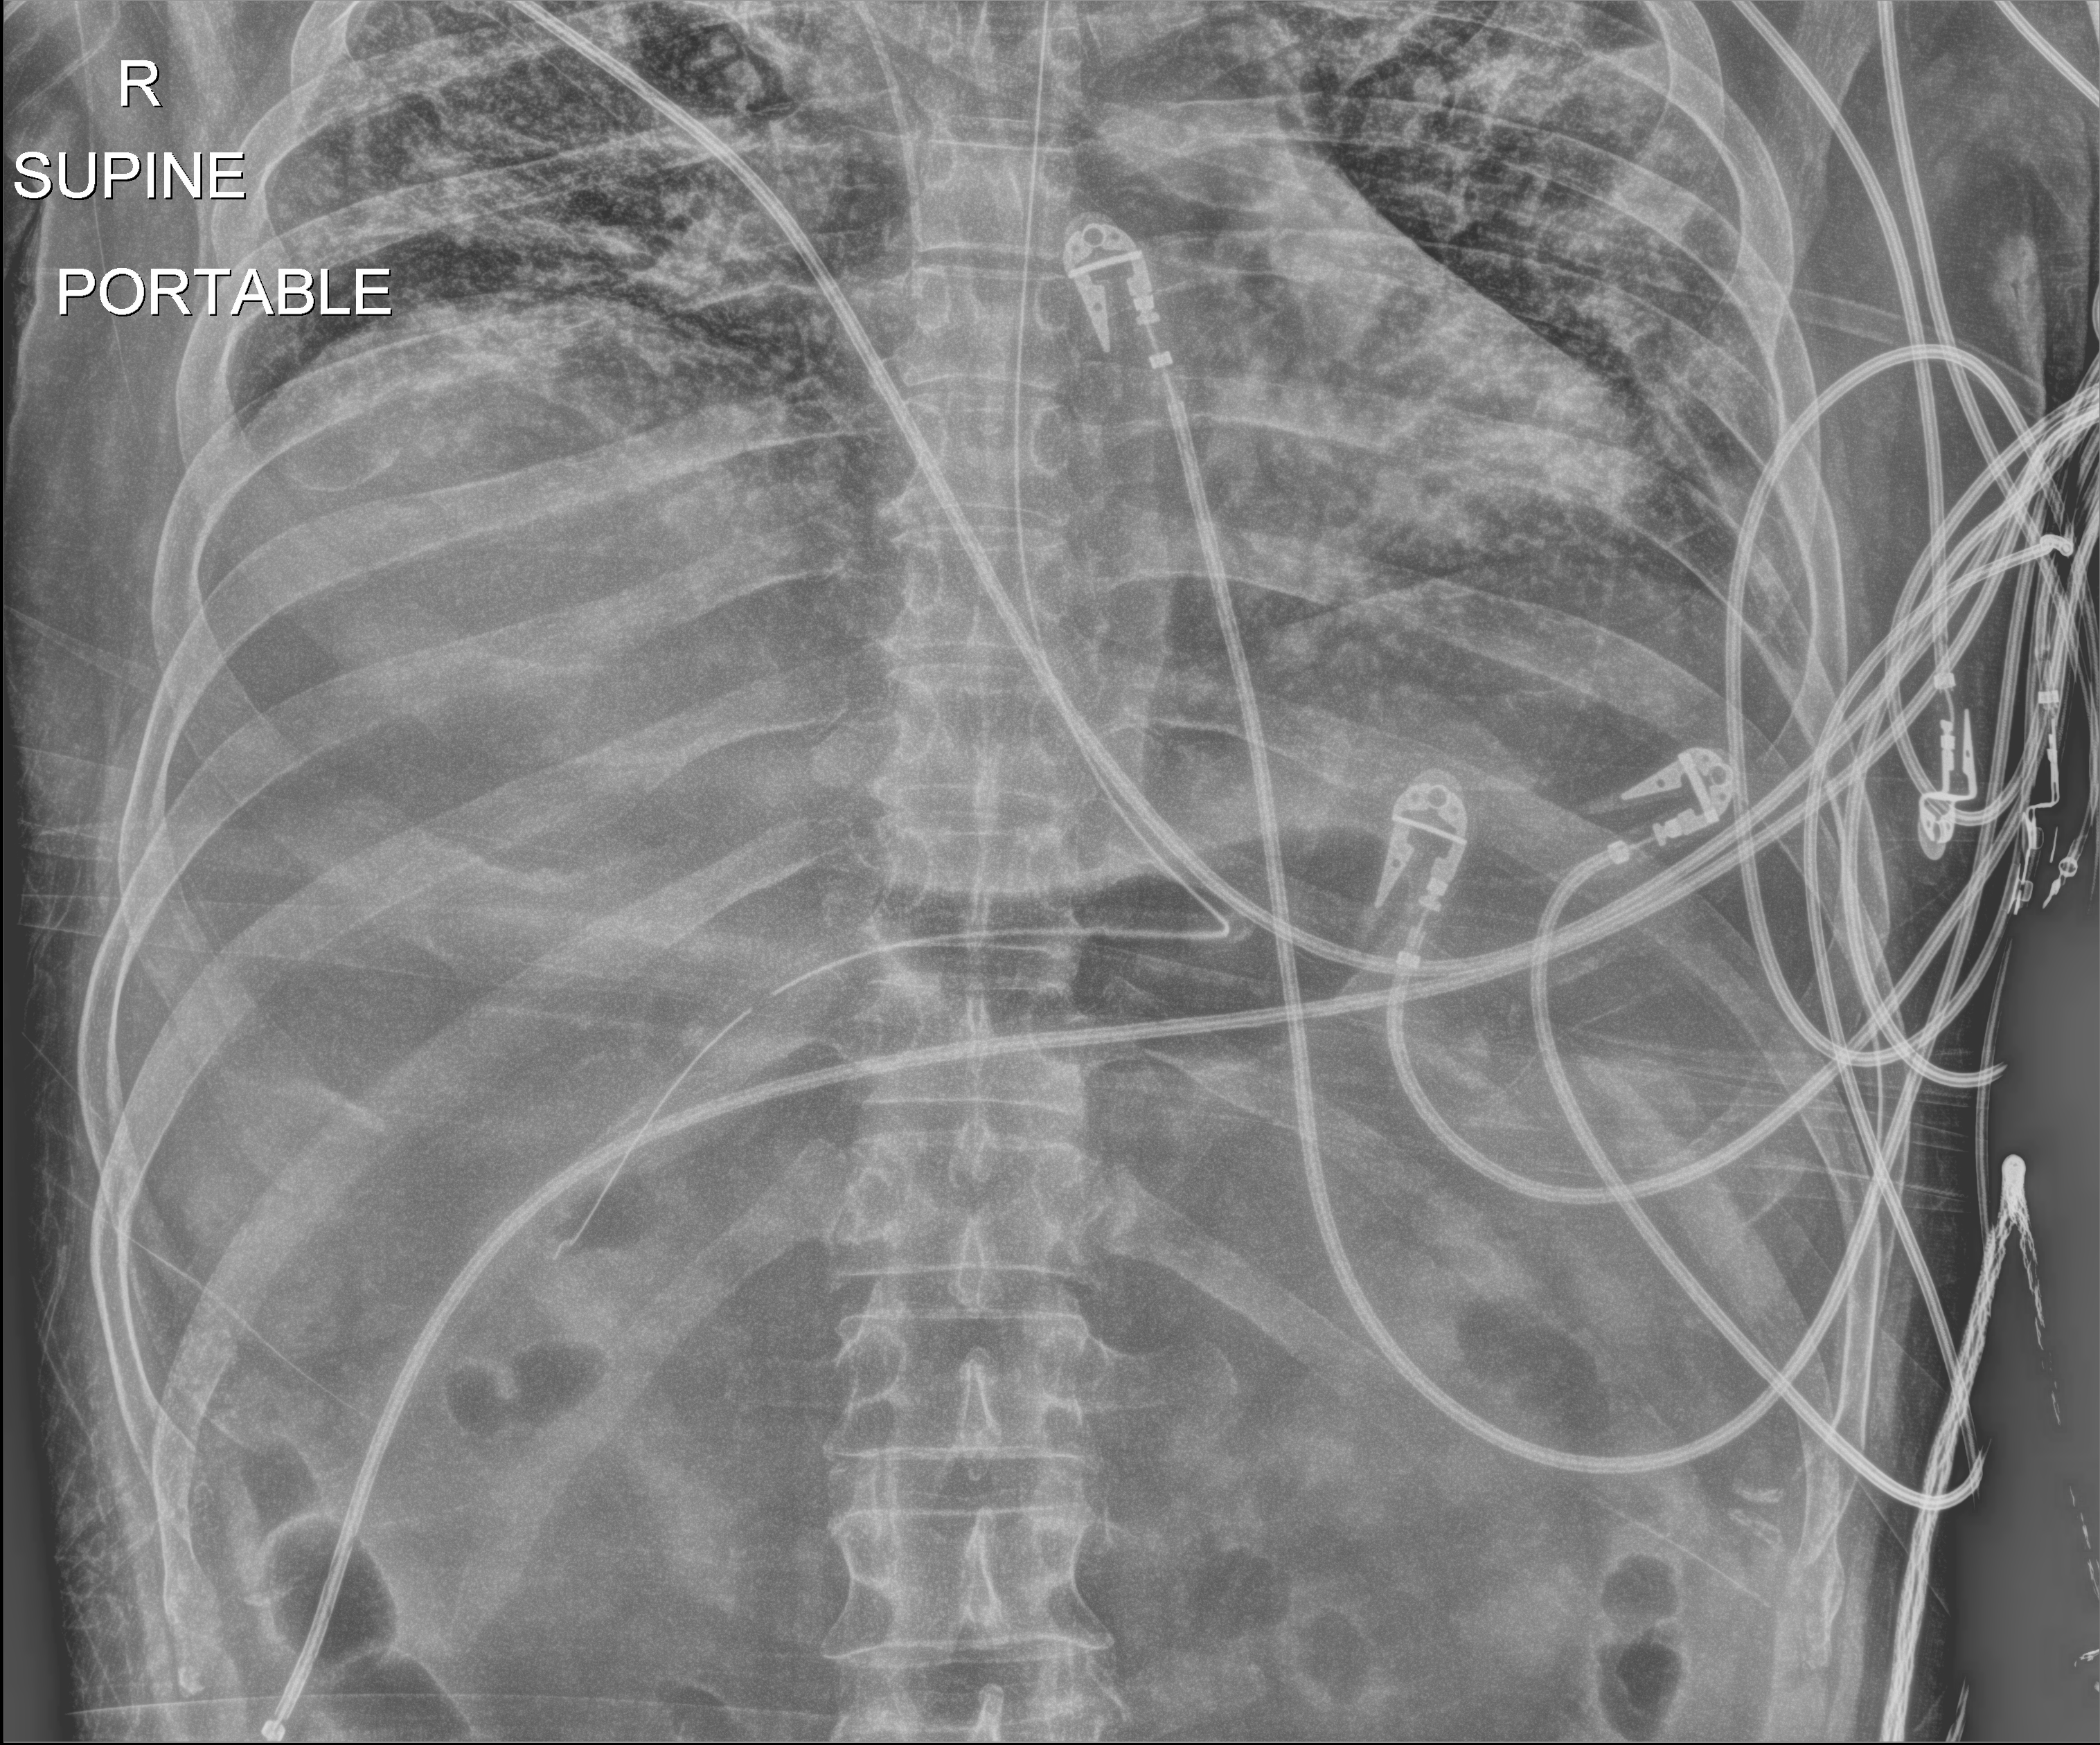
Portable chest radiograph. Male patient hospitalised with COVID-19, age 18–59 years.
From the hospital-stay record, not from the radiograph (when in the stay this image was taken is not recorded): admitted to intensive care during this hospital stay: yes; smoking status (admission record): never.